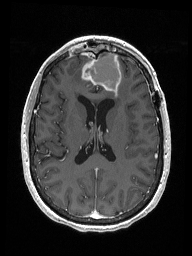
Brain MRI from a brain-tumour surgery series, one axial slice; slice 73 of 192 in the series (ordered by position); T1-weighted post-contrast; 1 mm slice thickness; 192 × 256 image matrix. Case-level facts recorded for this patient, not image findings: histopathology: Metastastic Carcinoma from Breast primary; tumour location: Right Frontal.
Annotated regions visible in this slice (expert manual segmentation):
- previous resection cavity: bounding box (x1, y1, x2, y2) in pixels: (86, 52, 122, 94)